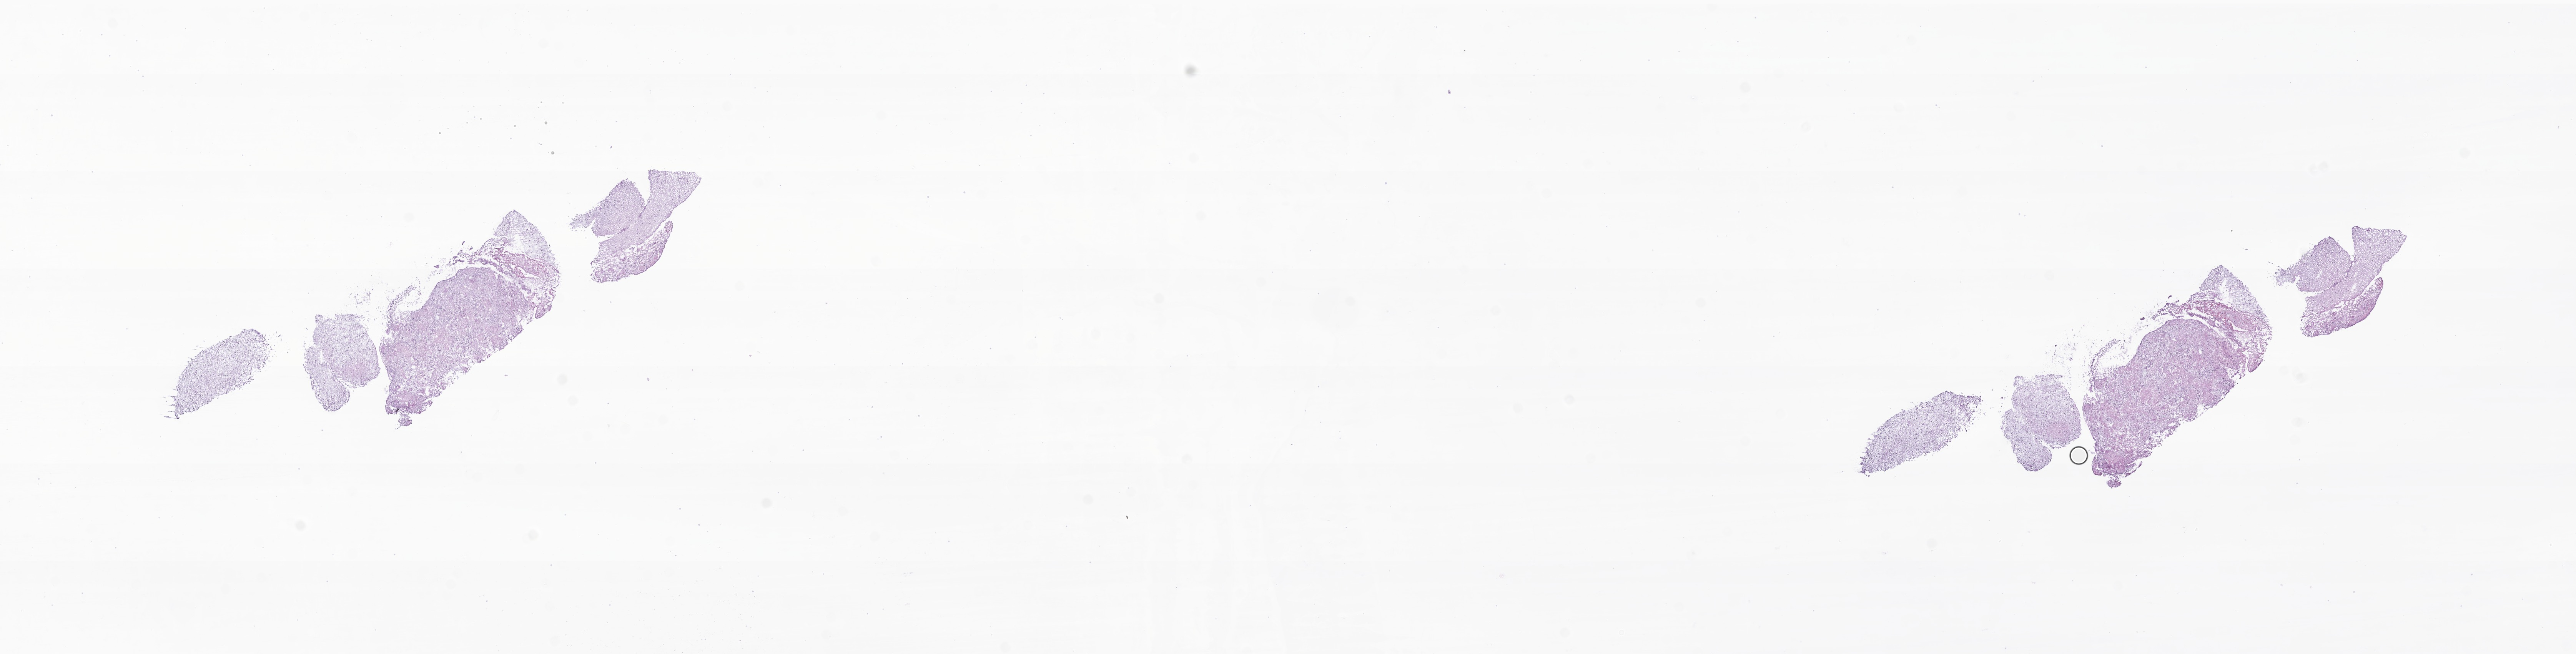
Digitized hematoxylin and eosin (H&E)-stained section of tumor tissue from the brain — shown as a low-resolution overview of the whole scanned area (about 28.3 x 7.2 mm). Frozen section (OCT-embedded). Patient male; age 50 months.
Recorded diagnosis: Pilocytic astrocytoma.